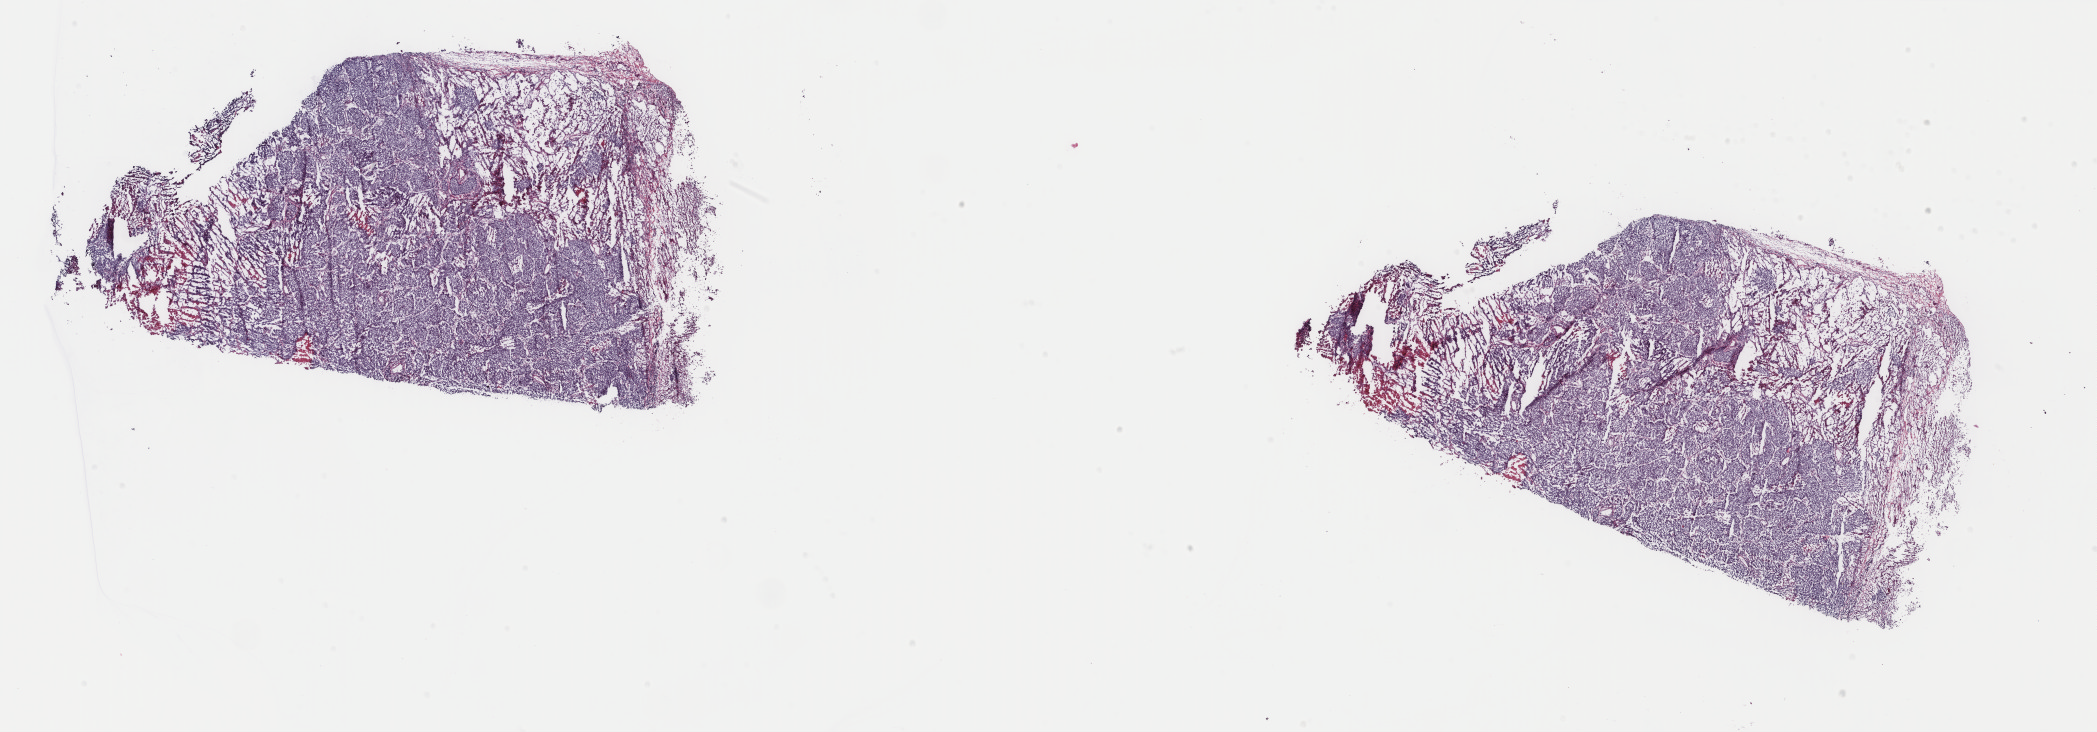
Digitized H&E-stained tissue section (whole slide) — shown as a low-resolution overview of the whole scanned area (about 33.3 x 11.6 mm, from a 40x scan). Frozen section from the top of the tissue portion. Primary tumour sample from the lung. Female patient; age at initial diagnosis 74 years. Composition of this section per pathologist review: tumour cells 80%, tumour nuclei 100%, normal cells 0%, stromal cells 10%, necrosis 10%. Infiltration values recorded for this section: lymphocyte infiltration 4%, monocyte infiltration 2%, neutrophil infiltration 2%.
- laterality: left
- AJCC pathologic stage: IIB
- diagnosis: Squamous cell carcinoma, NOS (lower lobe, lung)